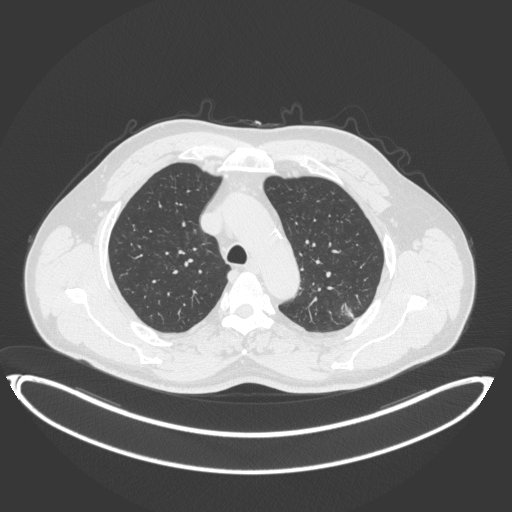
Chest CT, one axial slice. Position 274 of 399 along the scan axis. Lung window (W 1500 / L -600 HU). 1 mm slice thickness. 512 × 512 image matrix. Patient: male, 58 years. Case-level facts recorded for this patient, not image findings: clinical TNM (as recorded): T1c N0 M0; histopathological grade: G1-2.
Outlined on this slice (bounding box drawn by a radiologist):
- lung tumour (recorded histology: adenocarcinoma): bounding box (x1, y1, x2, y2) in pixels: (337, 299, 358, 321)